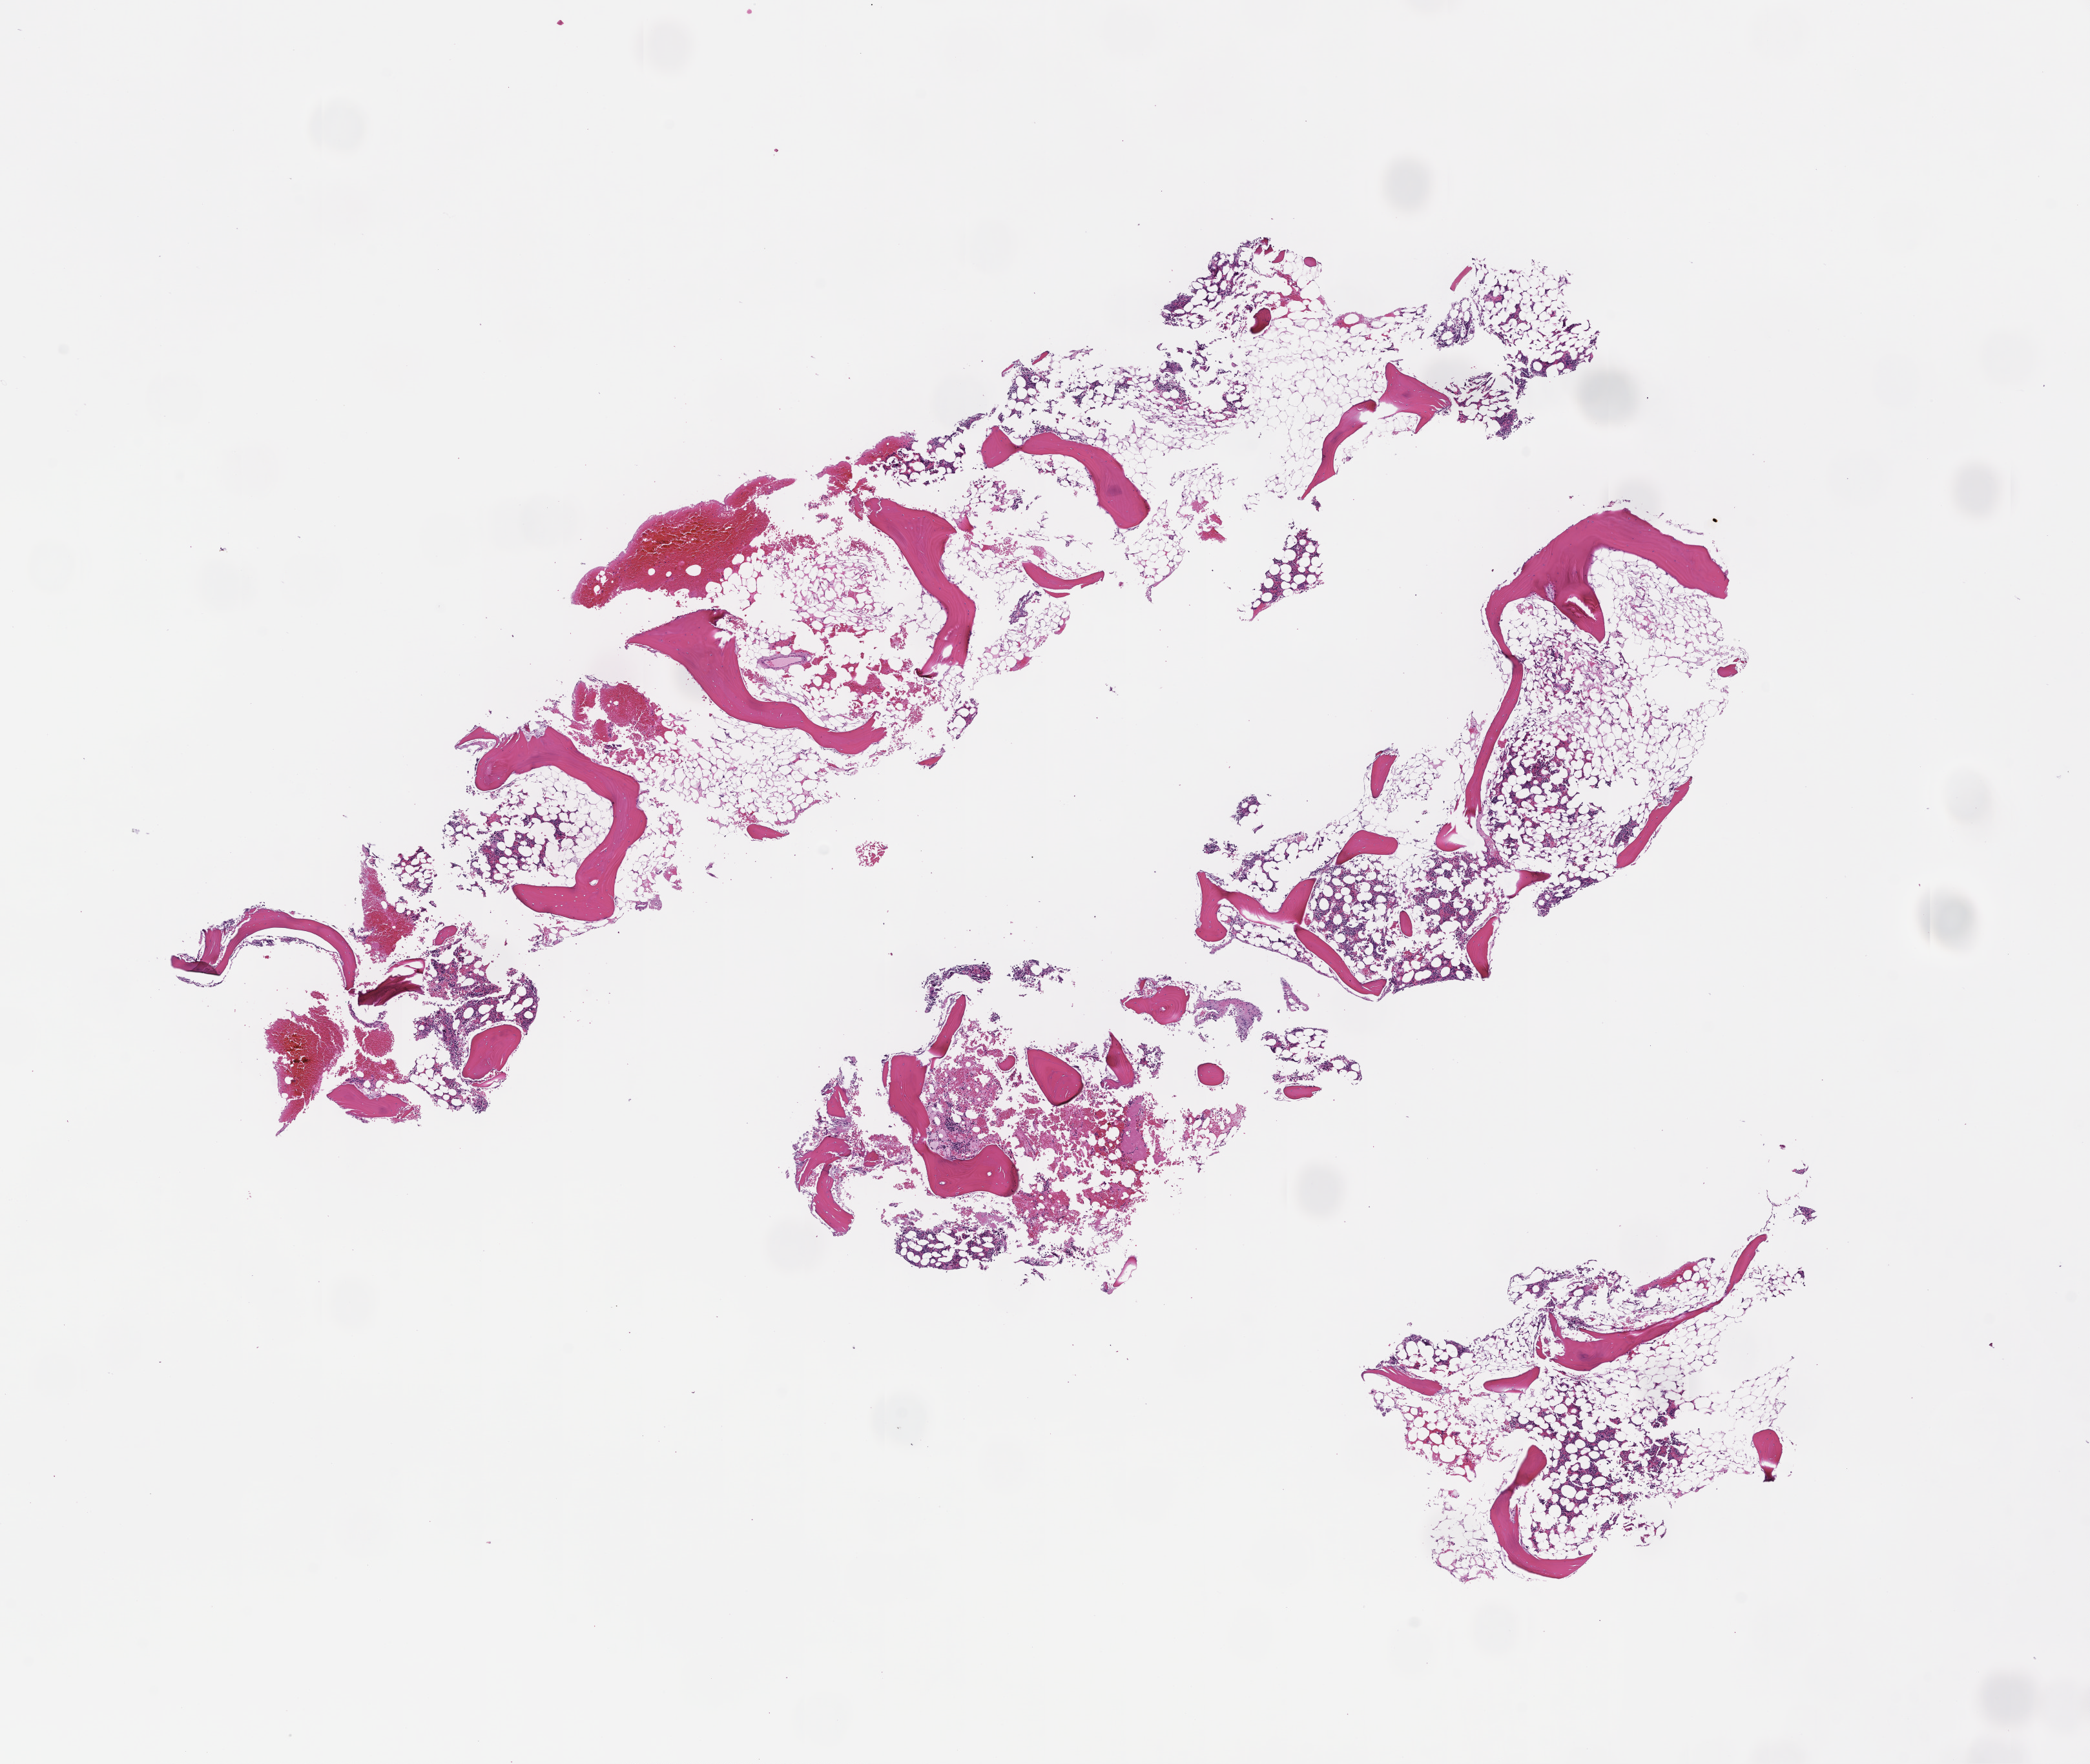
Whole-slide image, hematoxylin and eosin (H&E) stain, low-resolution overview of the scanned area, about 13.1 x 11.0 mm; FFPE section; site: bone marrow; archival tissue. Patient: male.
This section: primary tumour tissue. Diagnosis: Plasma Cell Myeloma.